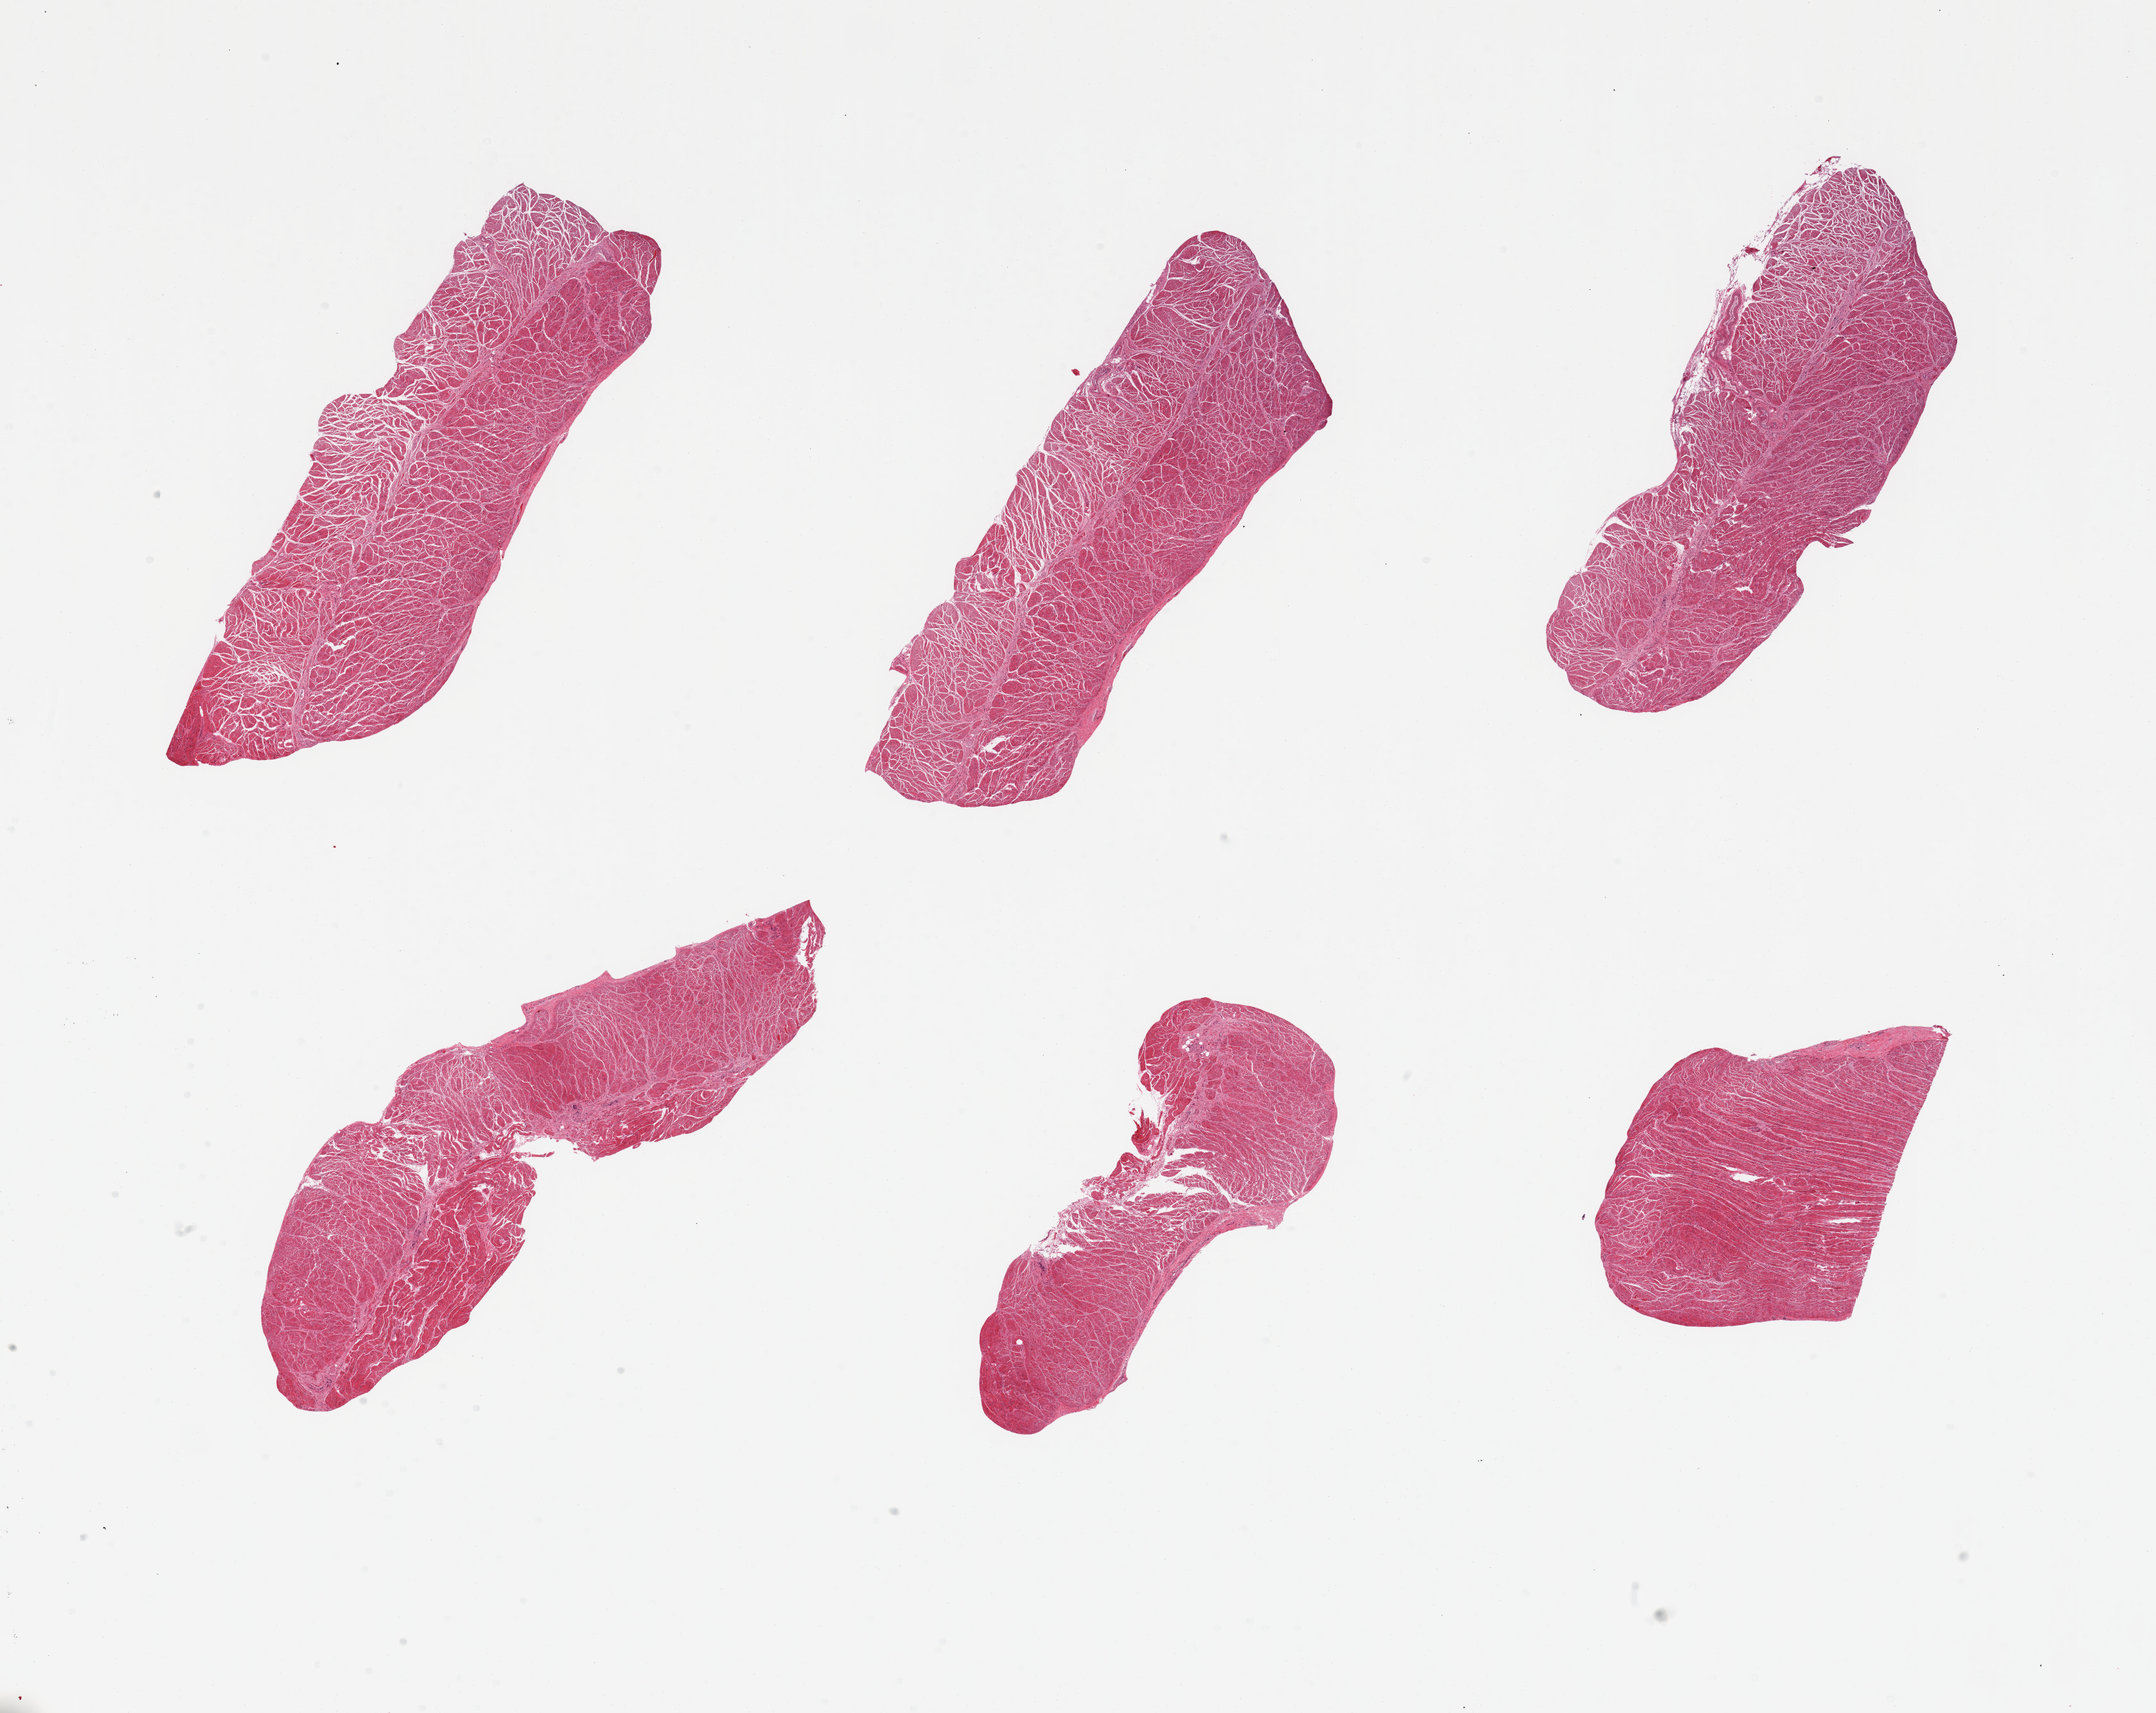
Digitized haematoxylin and eosin-stained section, whole scanned area (about 26.6 x 21.1 mm, acquisition: 20x scan) shown as a low-resolution overview, PAXgene-fixed paraffin-embedded (PFPE) section, sampled site (target tissue): gastroesophageal junction, donor tissue sample. Male donor.
Pathologist's review note for this sample: 6 pieces; well dissected muscularis.